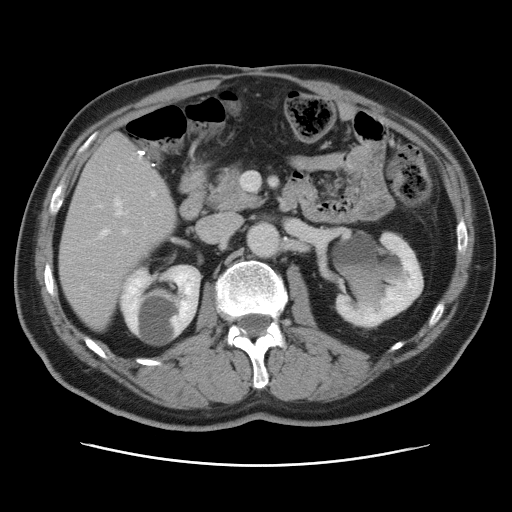
Contrast-enhanced abdominal CT, one axial slice. 120 kVp. Soft-tissue window (W 400 / L 40 HU). 5 mm slice thickness. 512 × 512 image matrix, field of view 370 × 370 mm. Male patient, age 69 years. From the clinical record (not read from this slice): diagnosis: colorectal cancer liver metastases, imaged before liver resection.
Structures marked on this image (manually delineated by an expert):
- hepatic veins: bounding box (x1, y1, x2, y2) in pixels: (81, 200, 121, 288)
- liver: (60, 135, 176, 328)
- planned liver remnant (the part of the liver to remain after resection): (60, 203, 176, 328)
- portal vein (with intrahepatic branches): (101, 193, 154, 278)